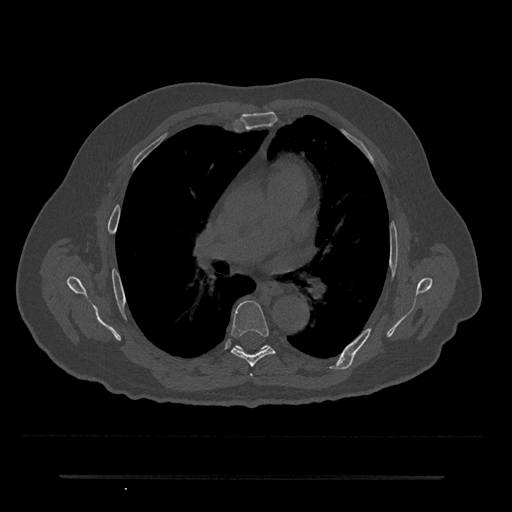
CT including the spine, one axial slice. Position 428 of 797 along the scan axis. Bone window (W 1800 / L 400 HU). 0.5 mm slice thickness. 512 × 512 image matrix, field of view 437 × 437 mm. Male patient, age 69 years. Case-level facts recorded for this patient, not image findings: primary cancer: prostate.
Annotated regions visible in this slice (semi-automatically segmented with operator editing):
- T6 vertebra: bounding box (x1, y1, x2, y2) in pixels: (230, 301, 275, 367)